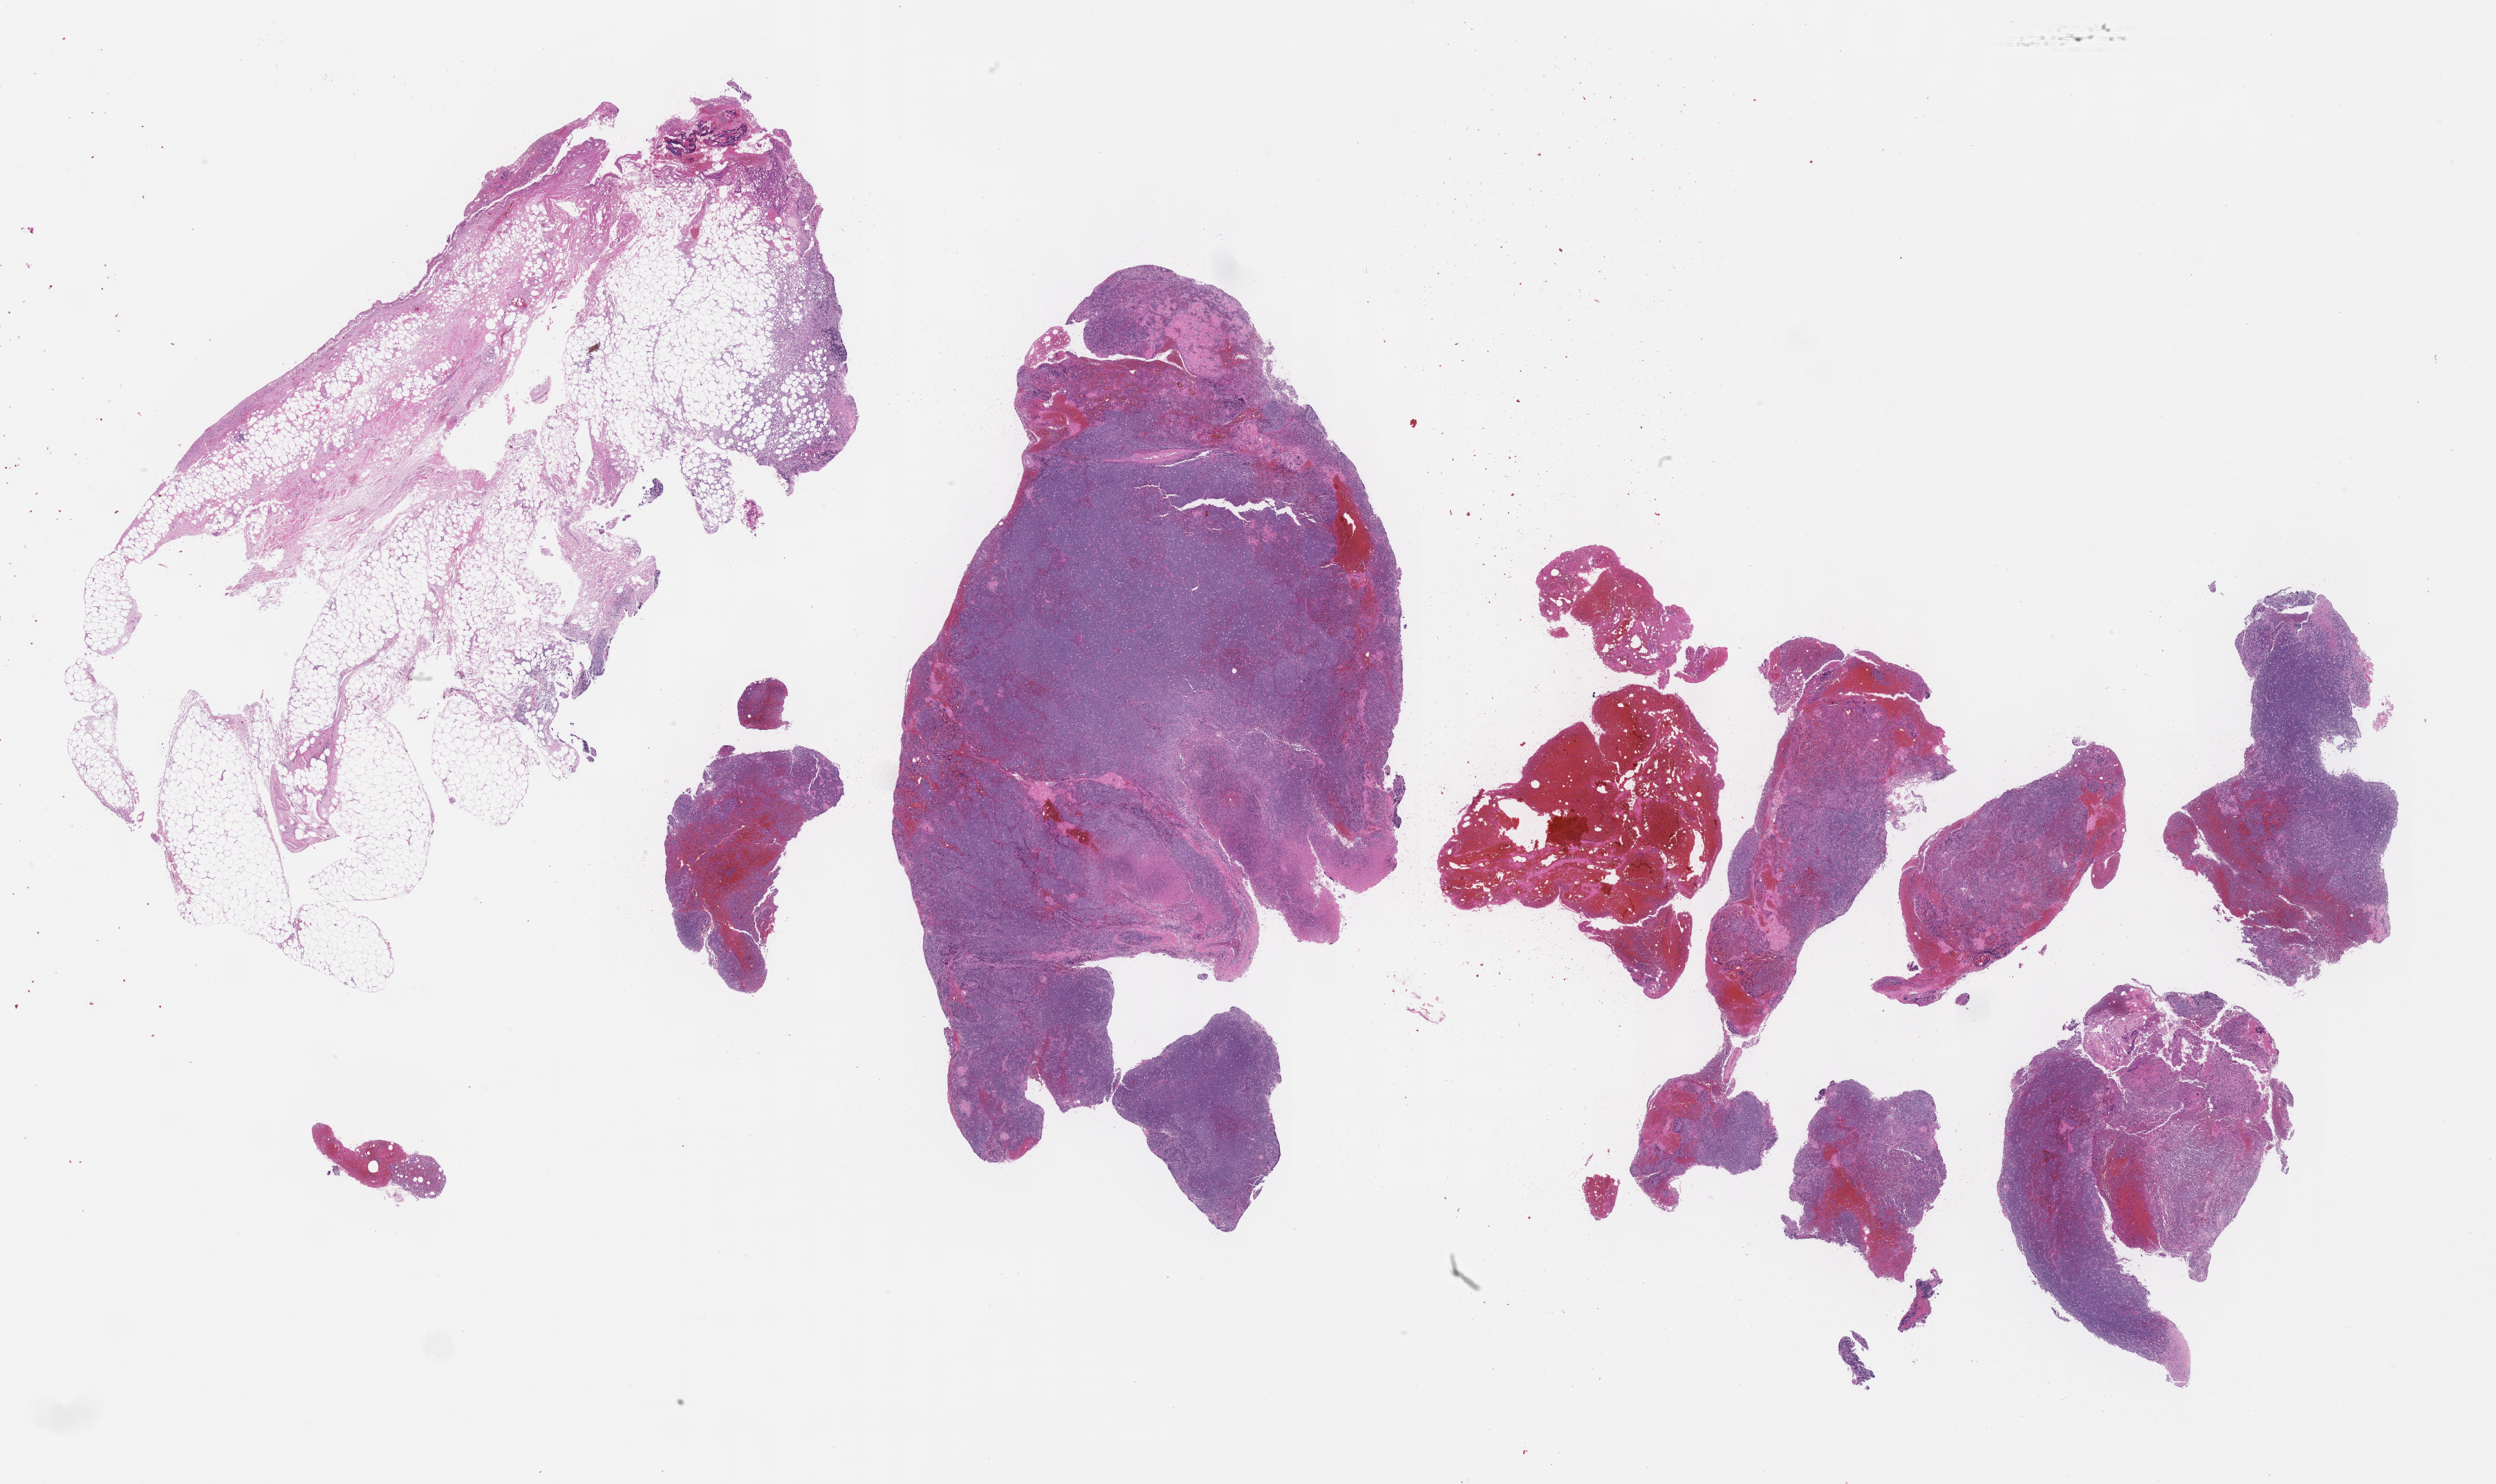
Whole-slide image, hematoxylin and eosin (H&E) stain, a low-resolution overview of the entire scanned area, about 29.2 x 17.4 mm, formalin-fixed, paraffin-embedded (FFPE) tissue, primary tumor, site: abdominal lymph node. Patient male; 27 years old. Pathologist review of this section (percent, as recorded): tumor cells 60%, tumor nuclei 90%.
Diagnosis: Burkitt lymphoma, NOS.